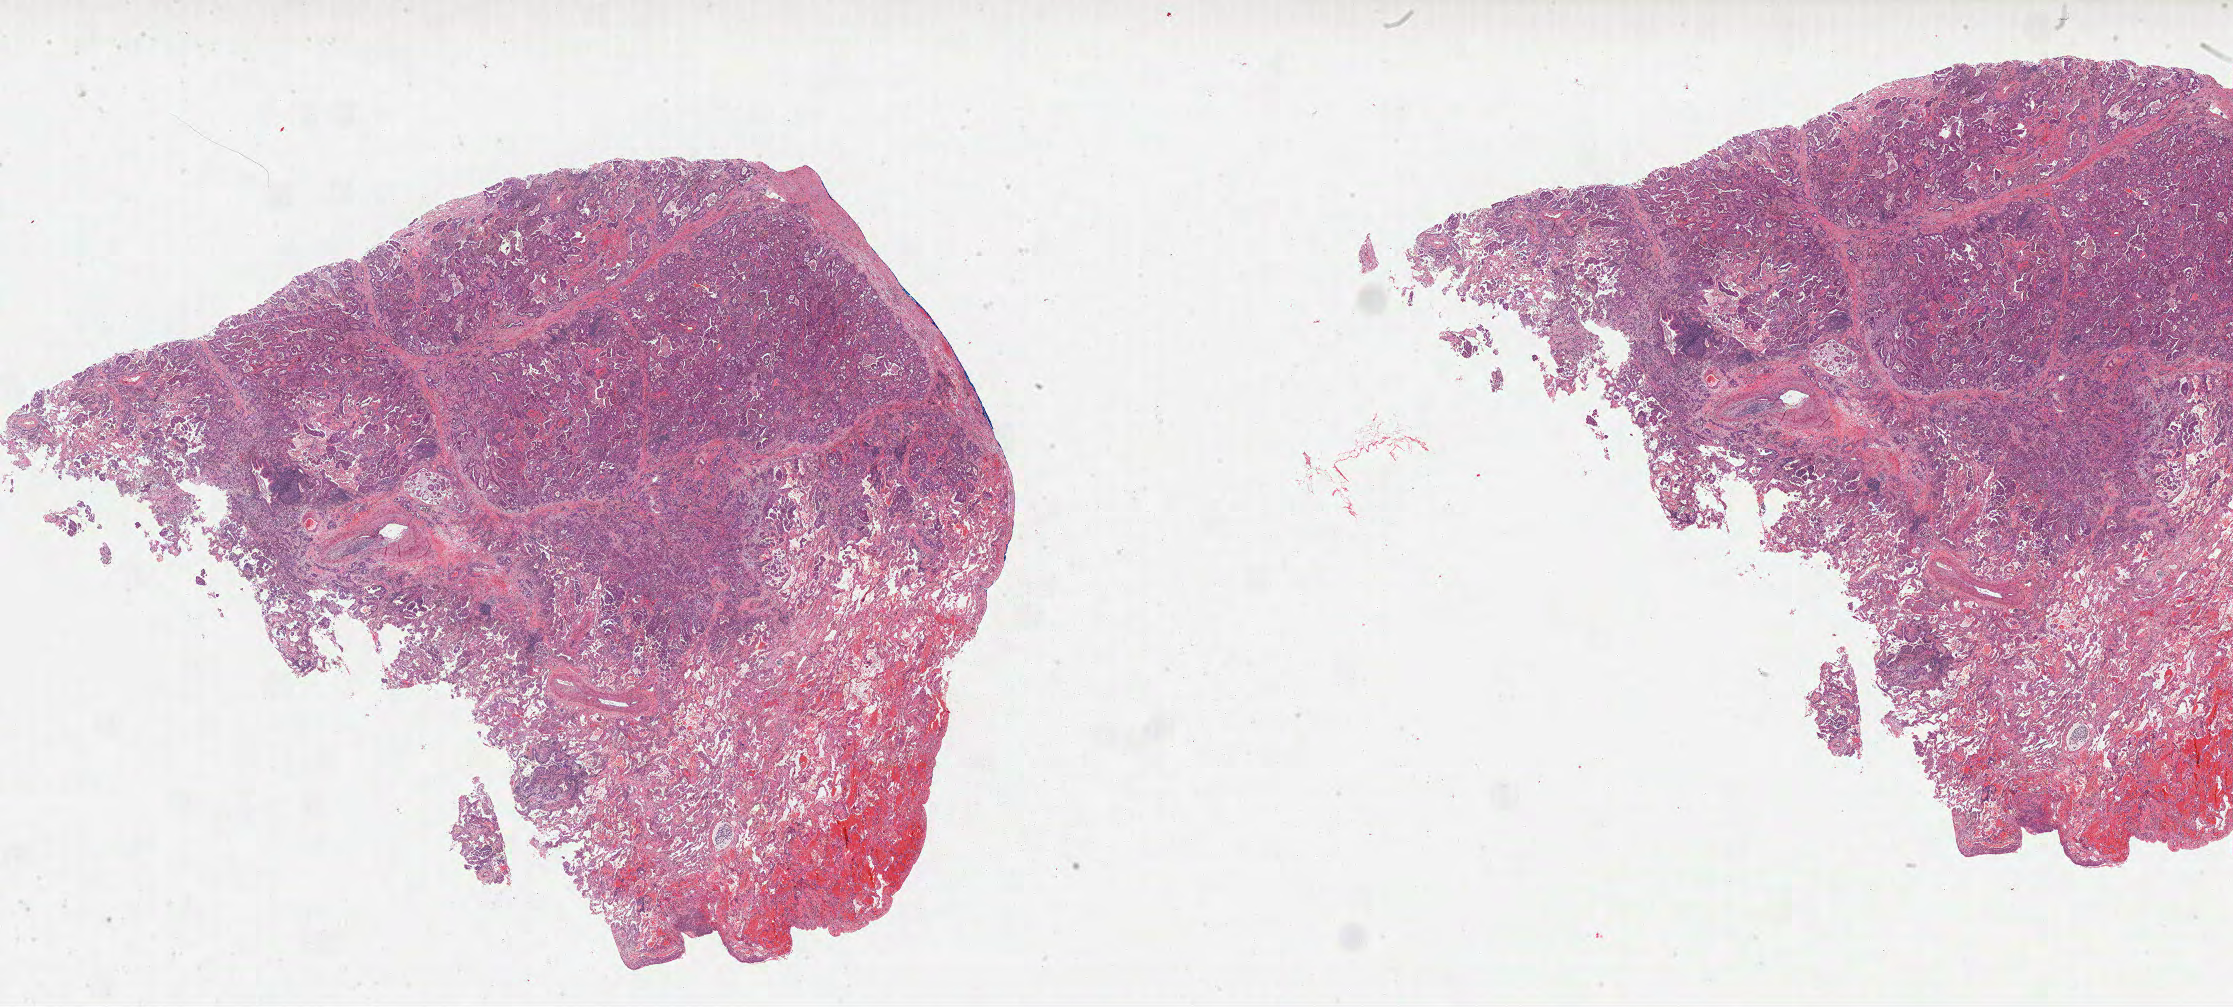
Whole-slide histology image, H&E-stained, low-resolution overview of the scanned area, about 36.0 x 16.2 mm (slide scanned at 40x), formalin-fixed paraffin-embedded (FFPE) diagnostic section, lung, primary tumour sample. Female, age 70 years at initial diagnosis.
AJCC pathologic stage: IIIA. Pathologic diagnosis: Adenocarcinoma, NOS (upper lobe, lung). TNM: T2b N2.